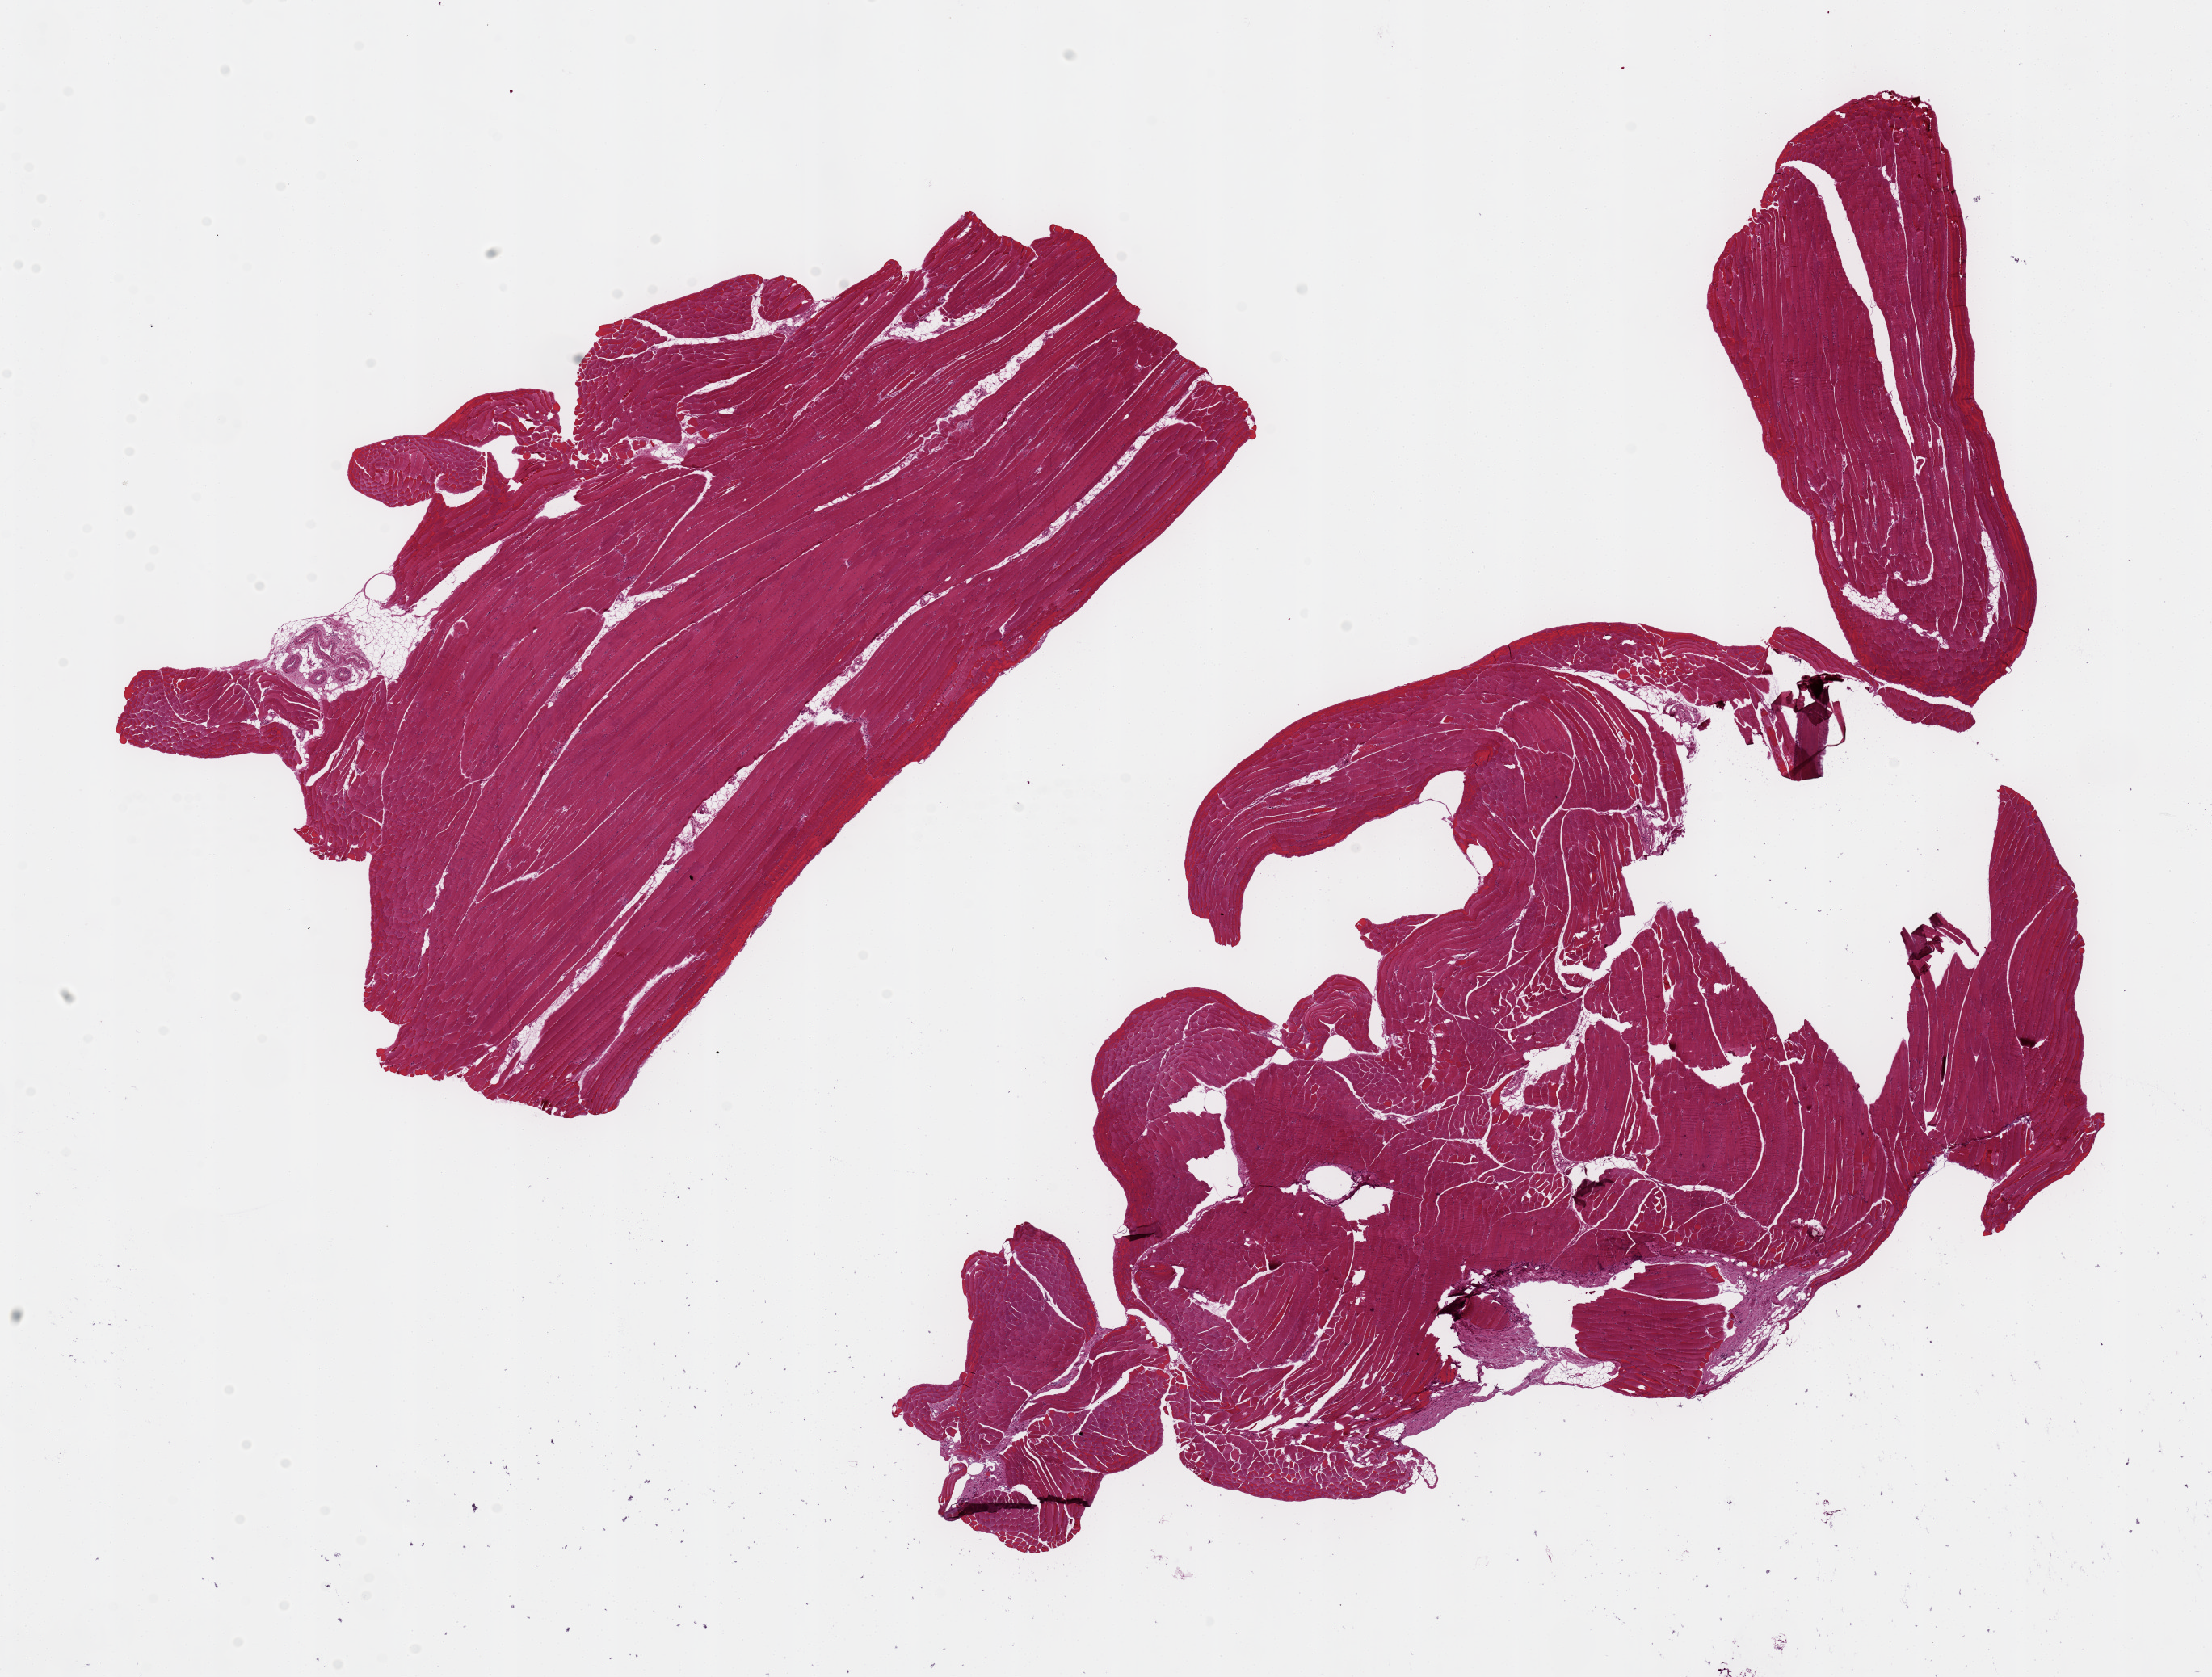
Digitized haematoxylin and eosin-stained section, brightfield, a low-resolution overview of the entire scanned area, about 21.7 x 16.4 mm. PAXgene-fixed, paraffin-embedded tissue. Sampled site (target tissue): skeletal muscle. Donor tissue sample. Donor sex: male.
• pathologist's review note for this sample: 2 pieces, 10x6 & 14x6 mm; minimal fat and stroma